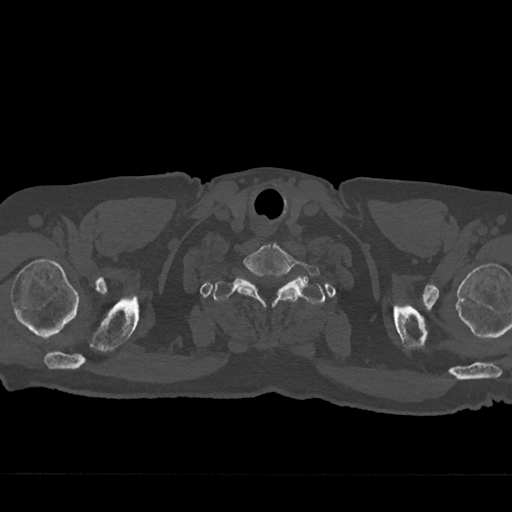
CT including the spine, one axial slice. Slice 678 of 797 in the series (ordered by position). Reconstruction kernel Br40s/3. Bone window (W 1800 / L 400 HU). 512 × 512 image matrix, field of view 377 × 377 mm. Patient: male, 75 years. Case-level facts recorded for this patient, not image findings: primary cancer: renal; vertebrae with lytic lesions (as recorded): T4.
Outlined on this slice (semi-automatically segmented with operator editing):
- T1 vertebra: bounding box (x1, y1, x2, y2) in pixels: (213, 278, 324, 304)